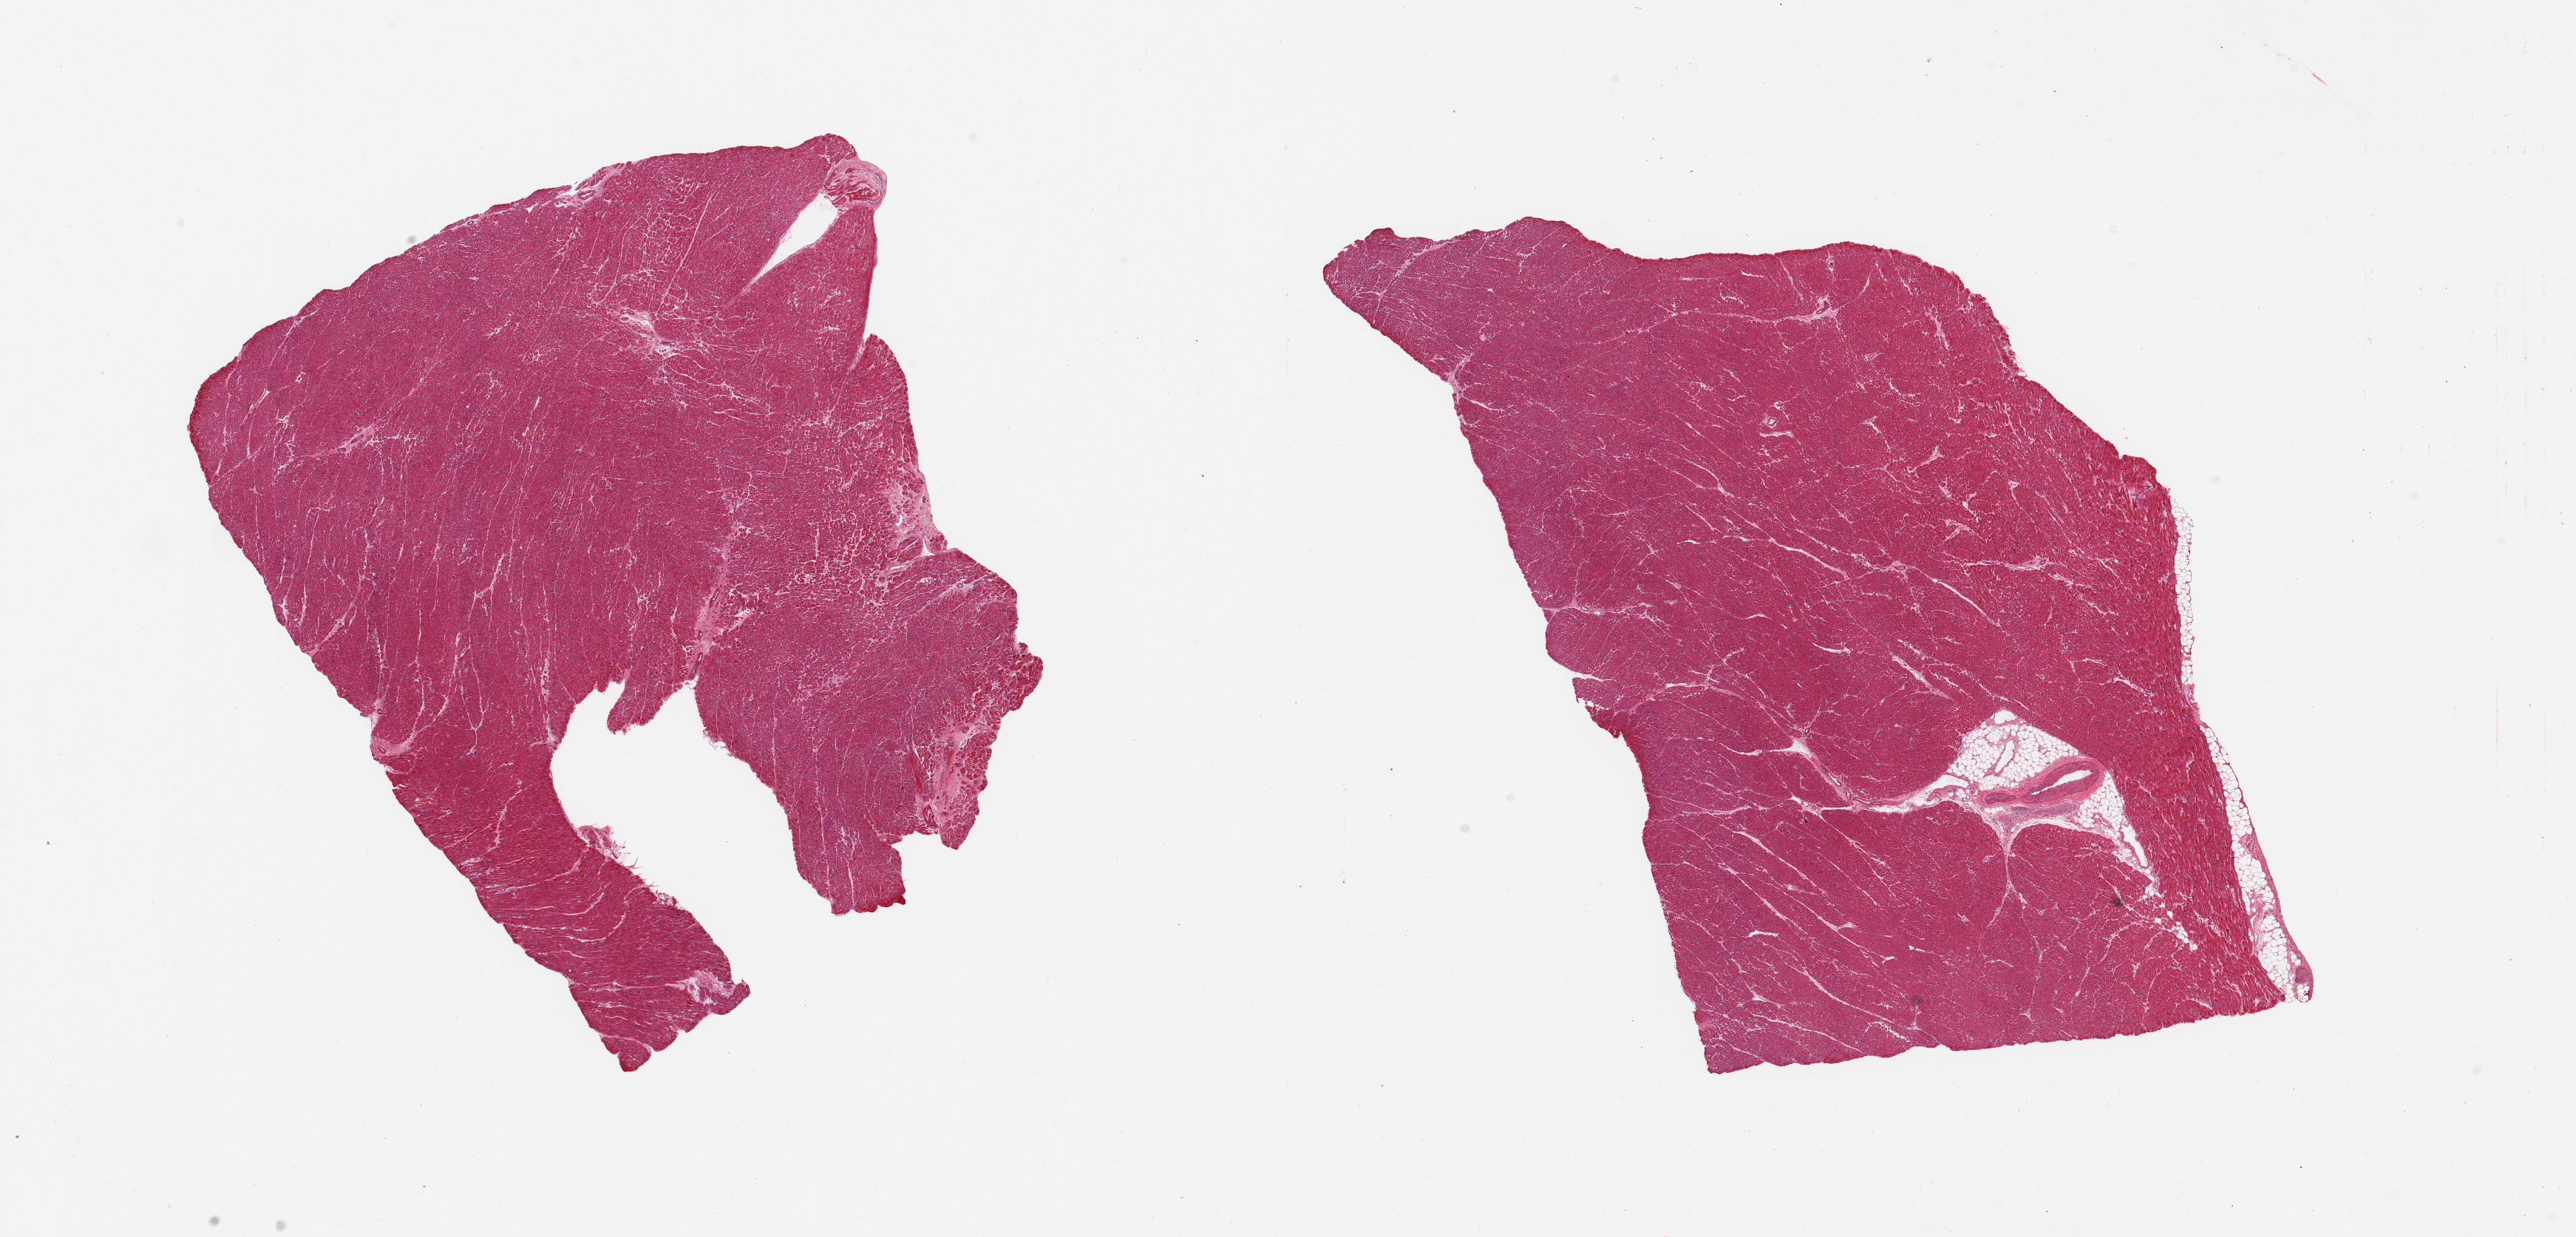
Whole-slide image, haematoxylin and eosin stain, brightfield, whole scanned area (about 27.6 x 13.2 mm, acquisition: 20x scan) shown as a low-resolution overview. PAXgene-fixed, paraffin-embedded tissue. Target tissue: heart. Tissue donor sample. Donor sex: male.
* reviewer comment on this tissue sample: 2 pieces; enlarged nuclei; few small patchy fibrous foci